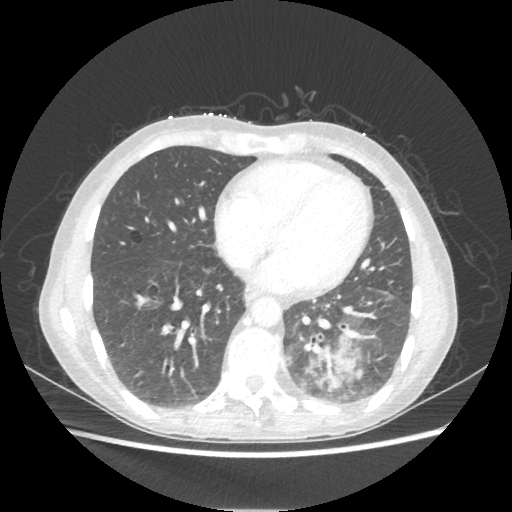
Chest CT, one axial slice; slice 84 of 221 in the series (ordered by position); reconstruction kernel STANDARD; 80 kVp; lung window (W 1500 / L -600 HU); 1.25 mm slice thickness; 512 × 512 image matrix. Female patient, age 53 years. From the clinical record (not read from this slice): clinical TNM (as recorded): T3 N0 M0.
Structures marked on this image (bounding box drawn by a radiologist):
- lung tumour (recorded histology: adenocarcinoma): bounding box (x1, y1, x2, y2) in pixels: (308, 342, 356, 390)